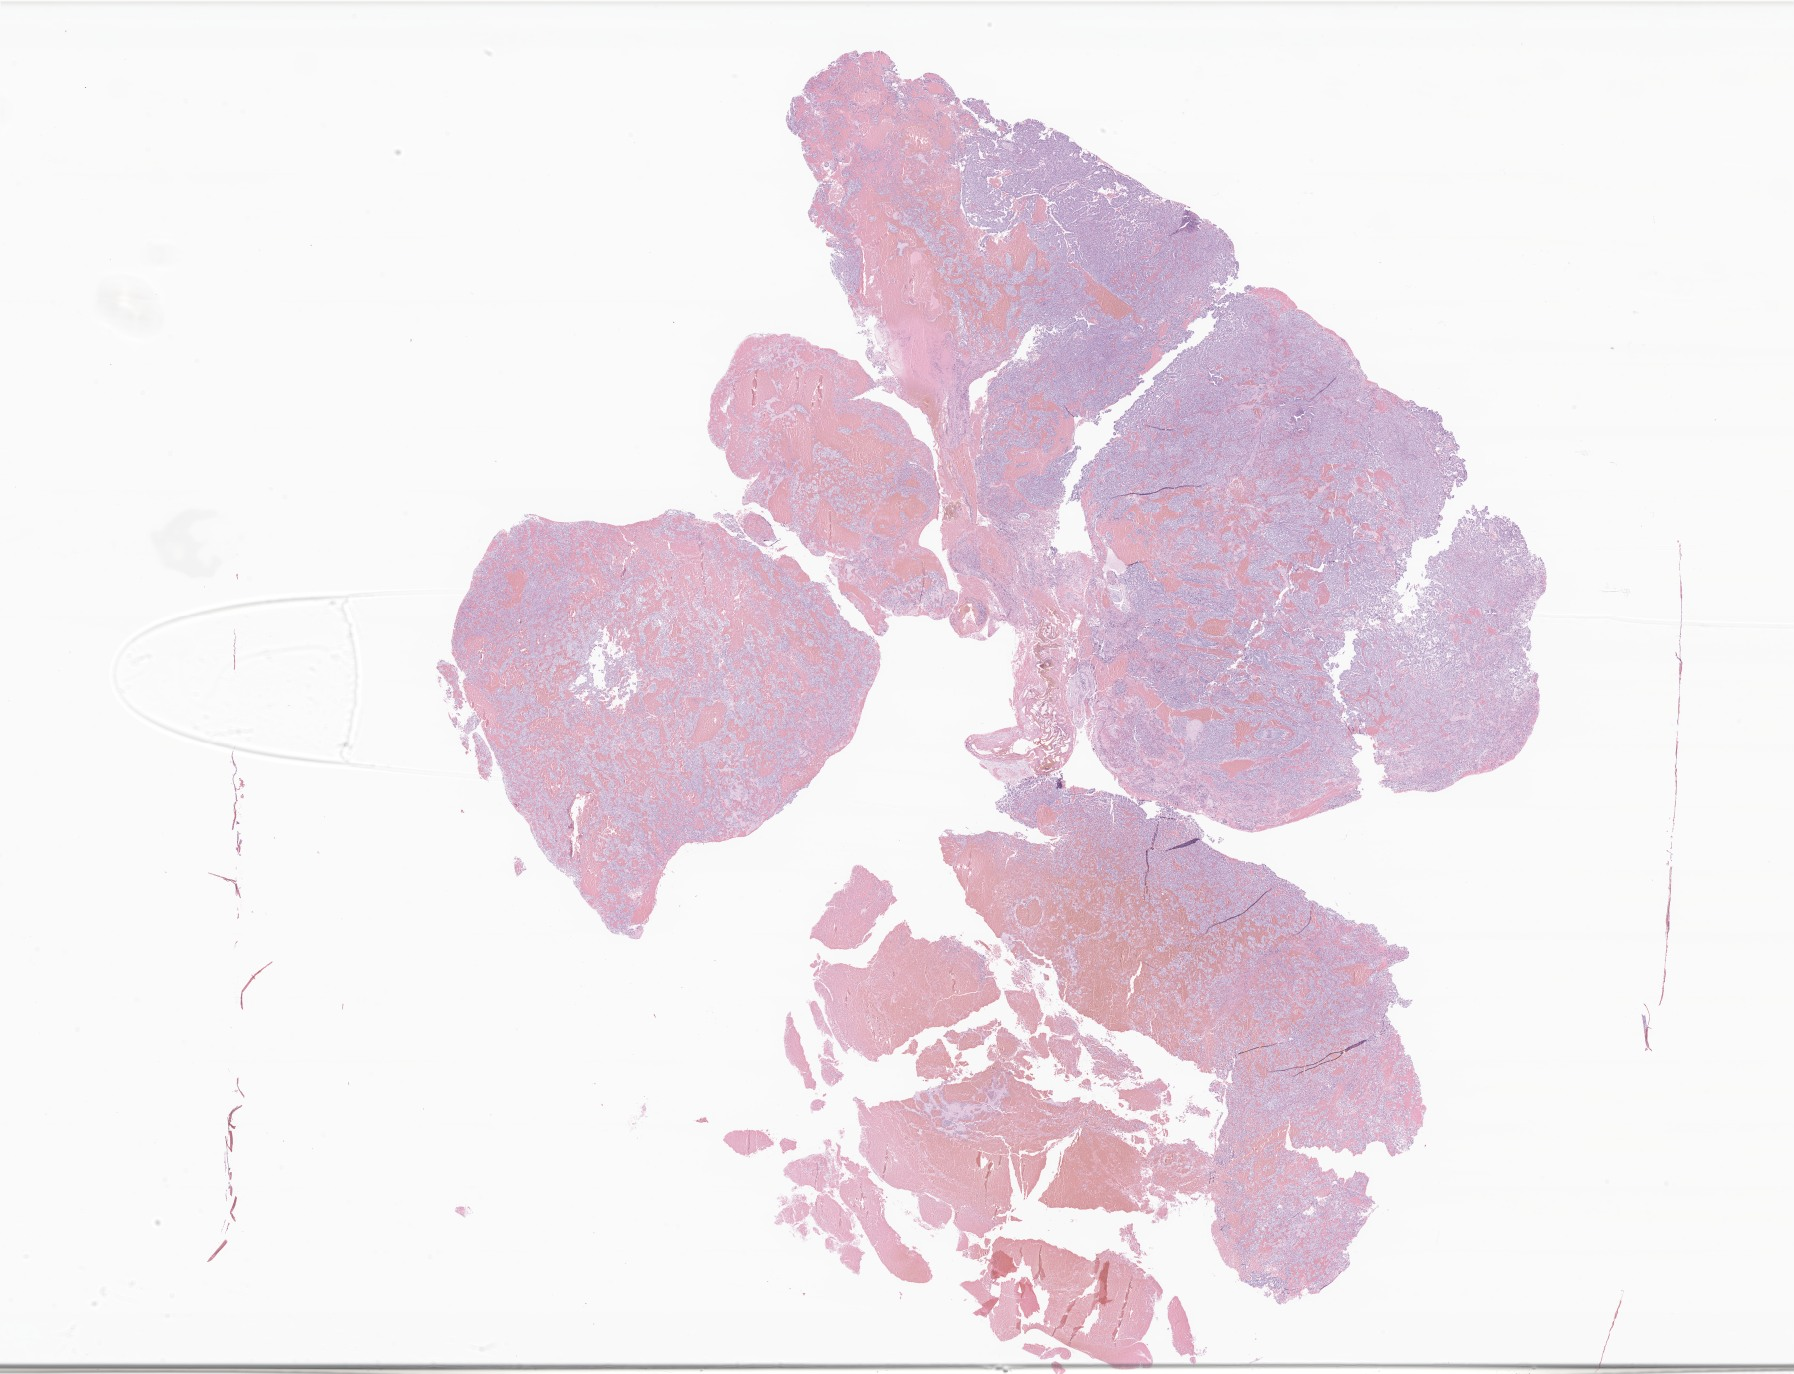
Digitized H&E-stained section of tumor tissue from the brain, low-resolution overview of the scanned area, about 30.3 x 23.2 mm. FFPE section. Male patient, age 141 months (11 years 9 months).
* diagnosis (ICD-O-3 morphology term): Glioma, malignant